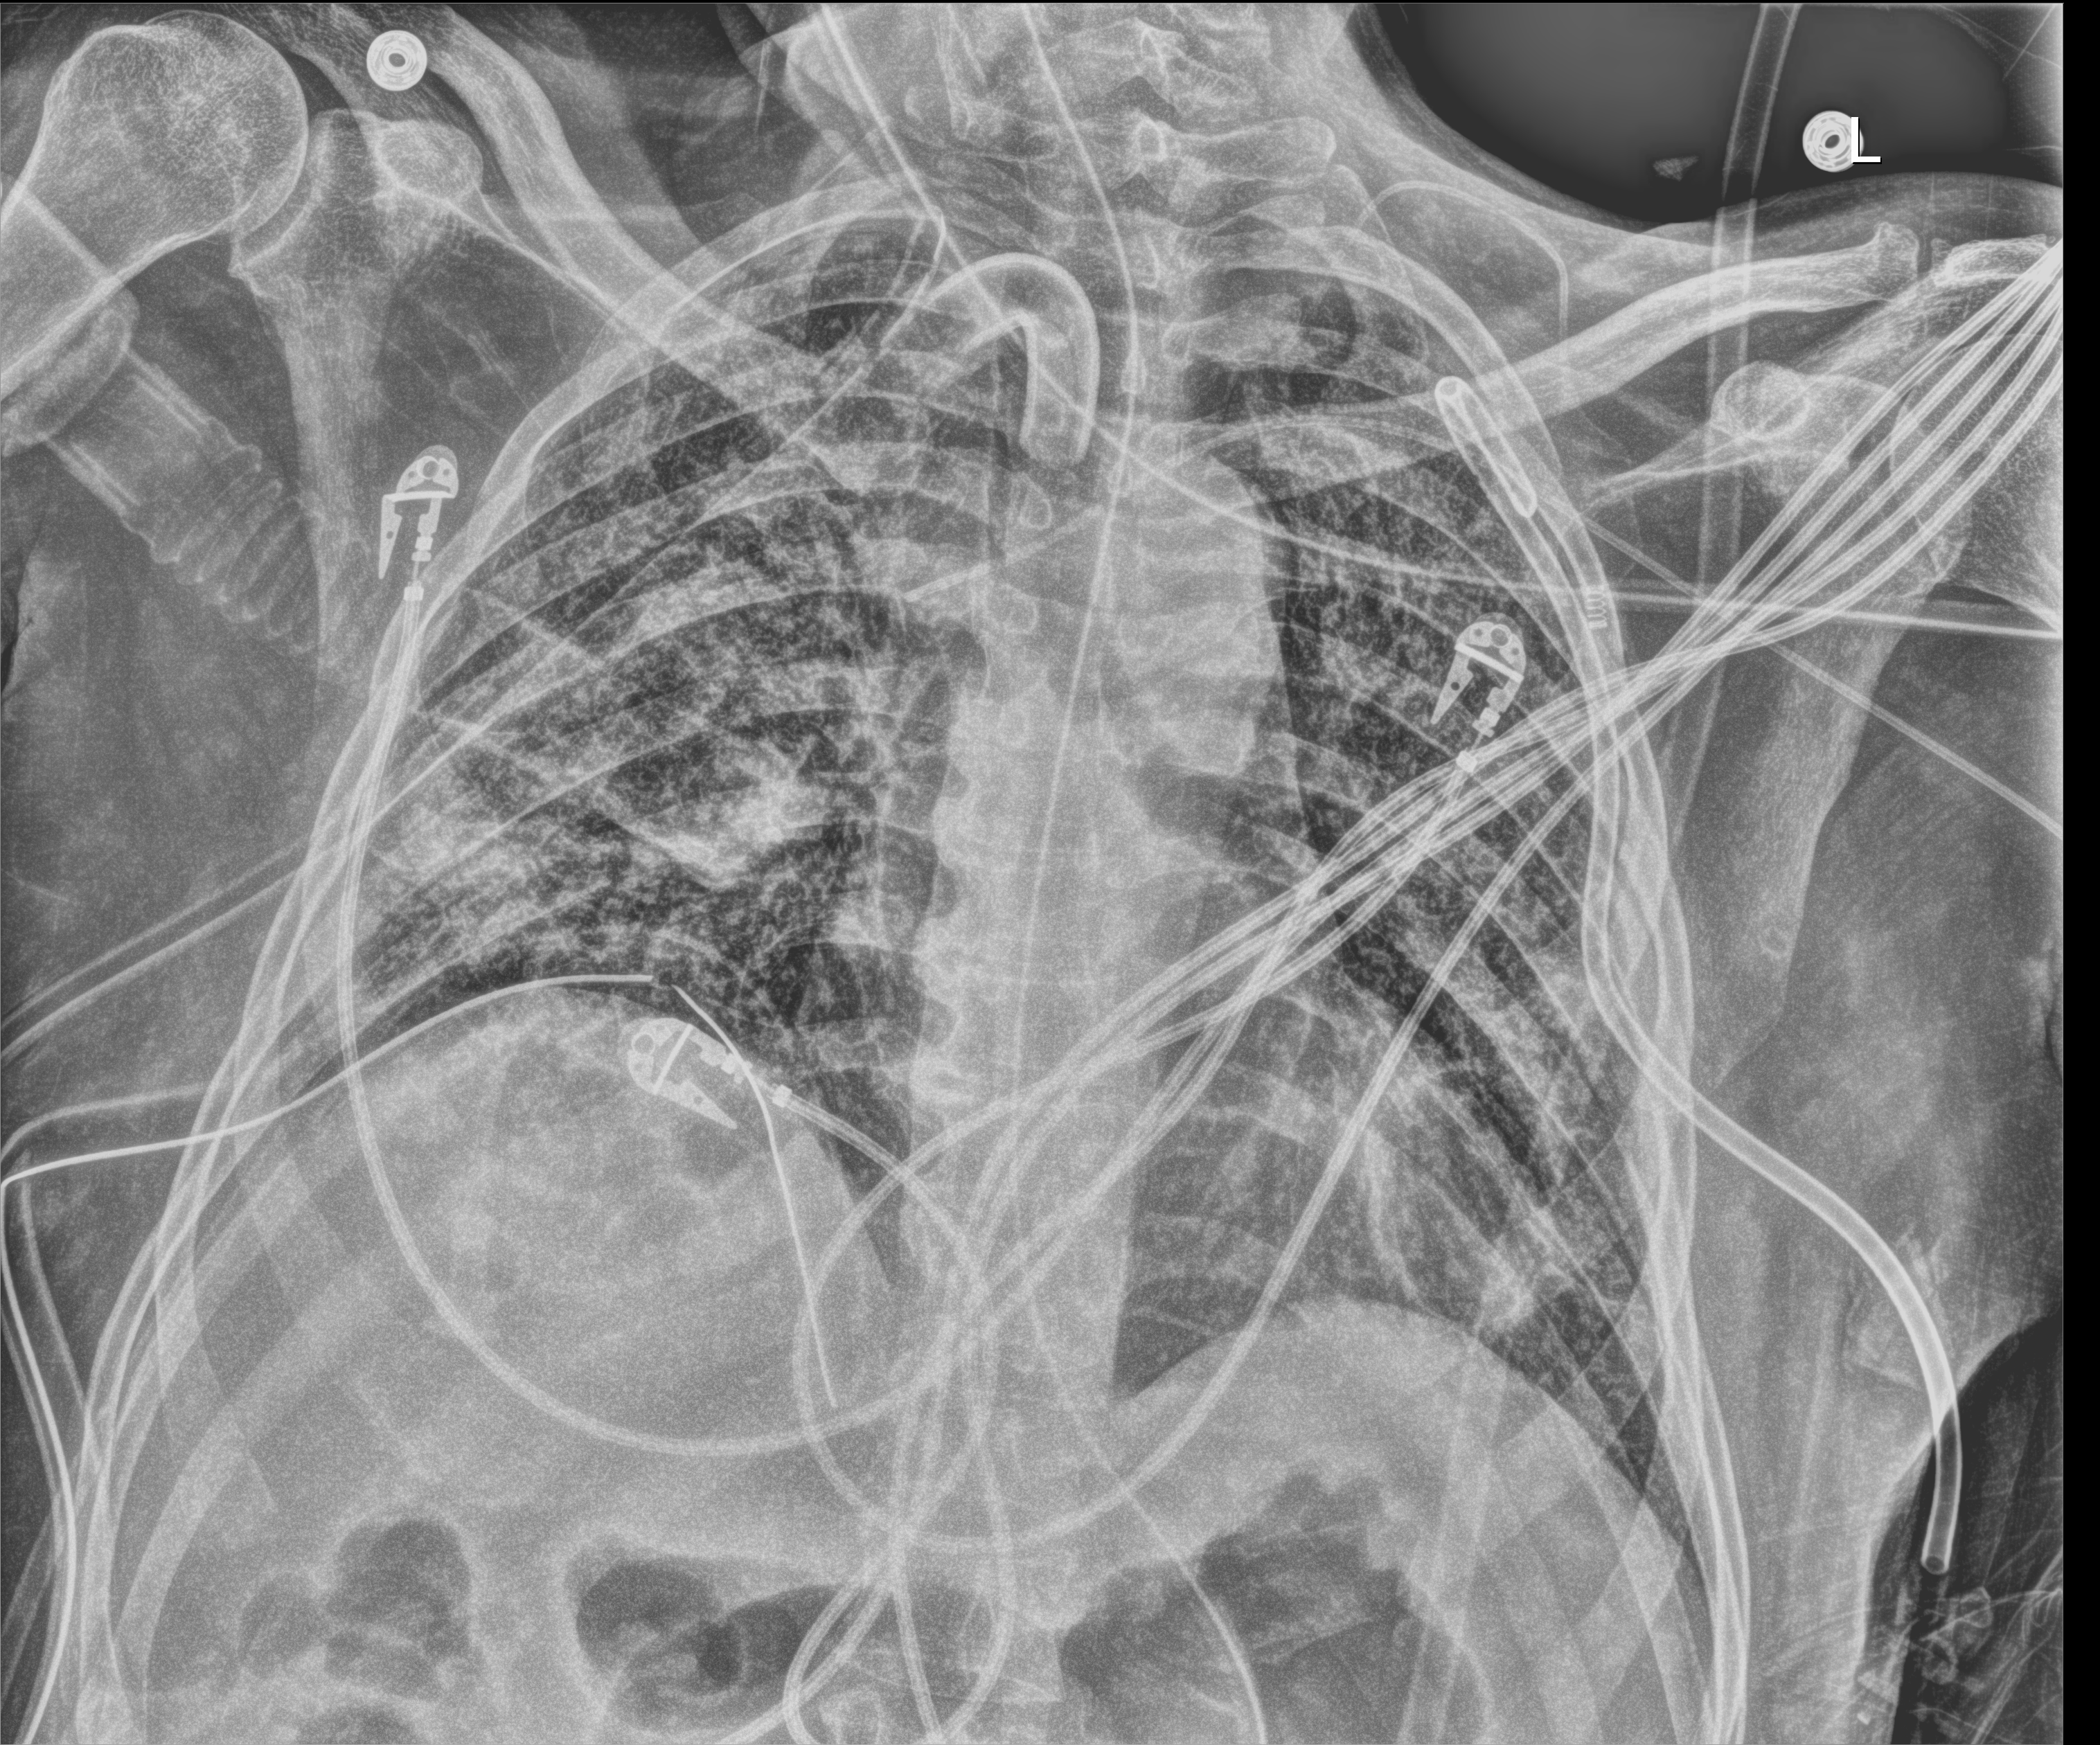
Bedside chest radiograph (digital radiography); anteroposterior (AP) projection. Male patient hospitalised with COVID-19, age 18–59 years.
Hospital-stay facts (about this admission, not read from this image; timing relative to this image not recorded): length of hospital stay: 83 days.